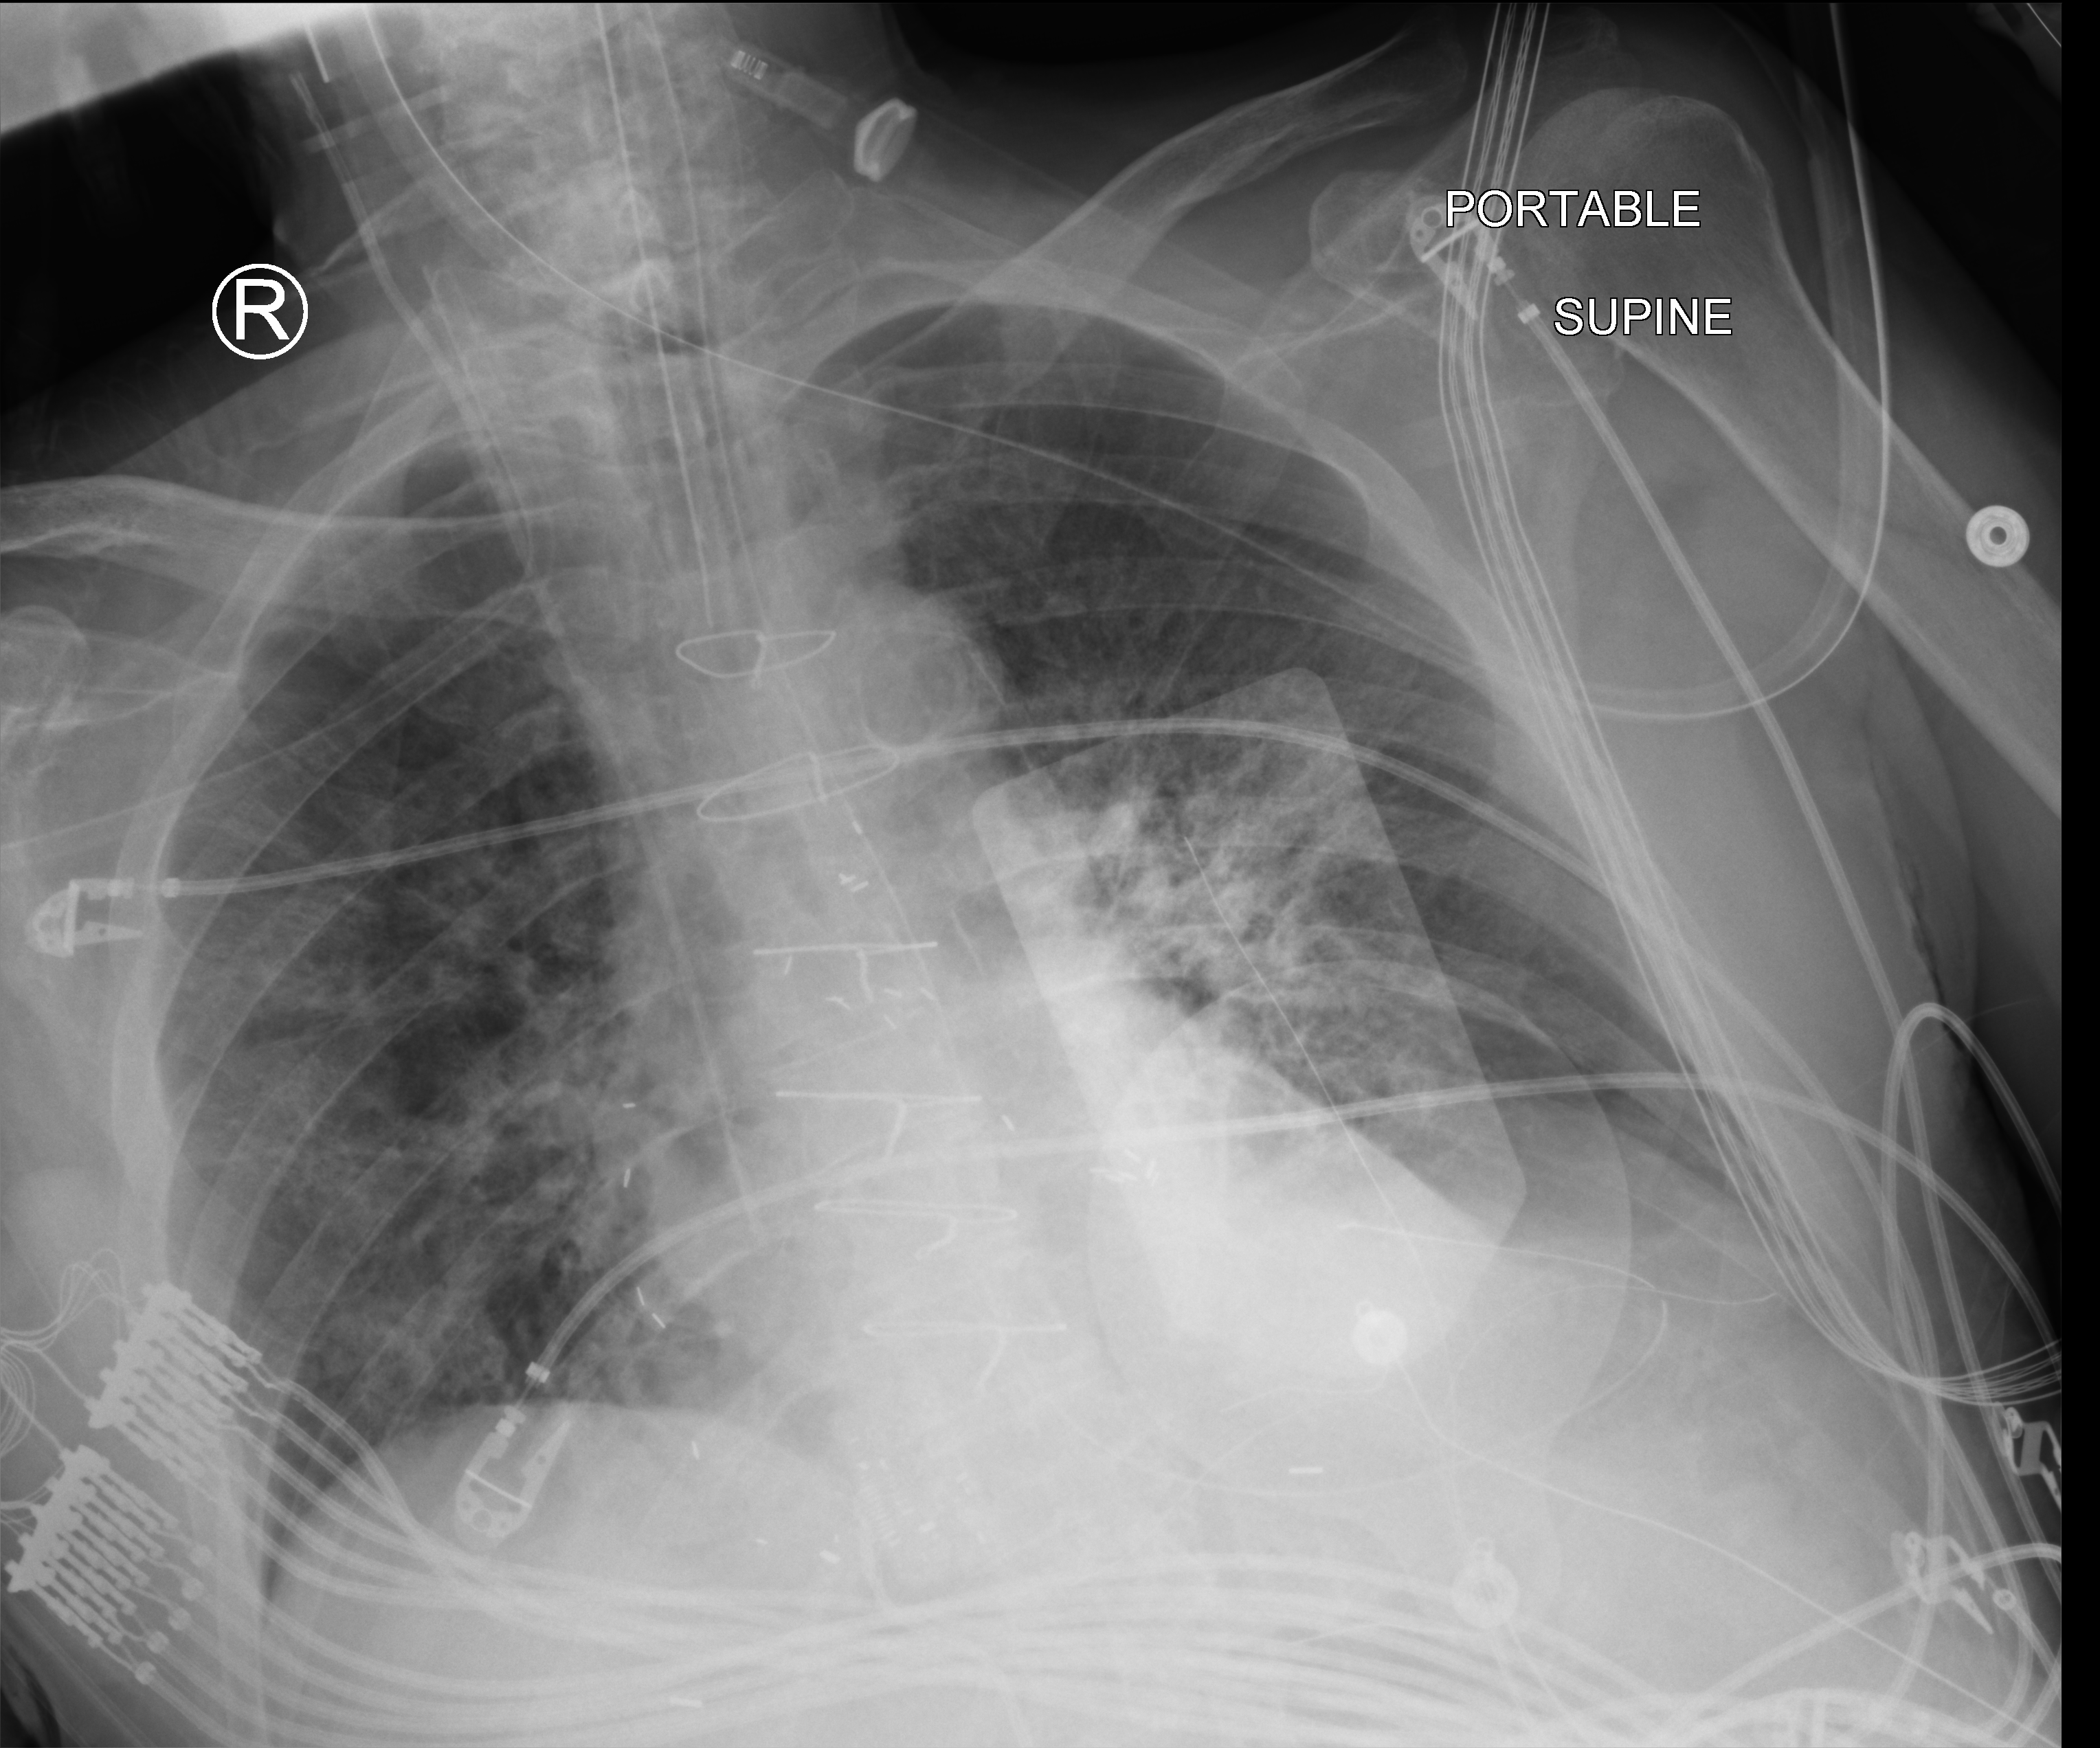
Bedside chest radiograph (computed radiography), anteroposterior (AP) projection. Patient hospitalised with COVID-19; male, aged 75–90 years.
From the hospital-stay record, not from the radiograph (when in the stay this image was taken is not recorded):
- admitted to intensive care during this hospital stay: yes
- mechanically ventilated during this hospital stay: yes
- hypertension (admission record): yes